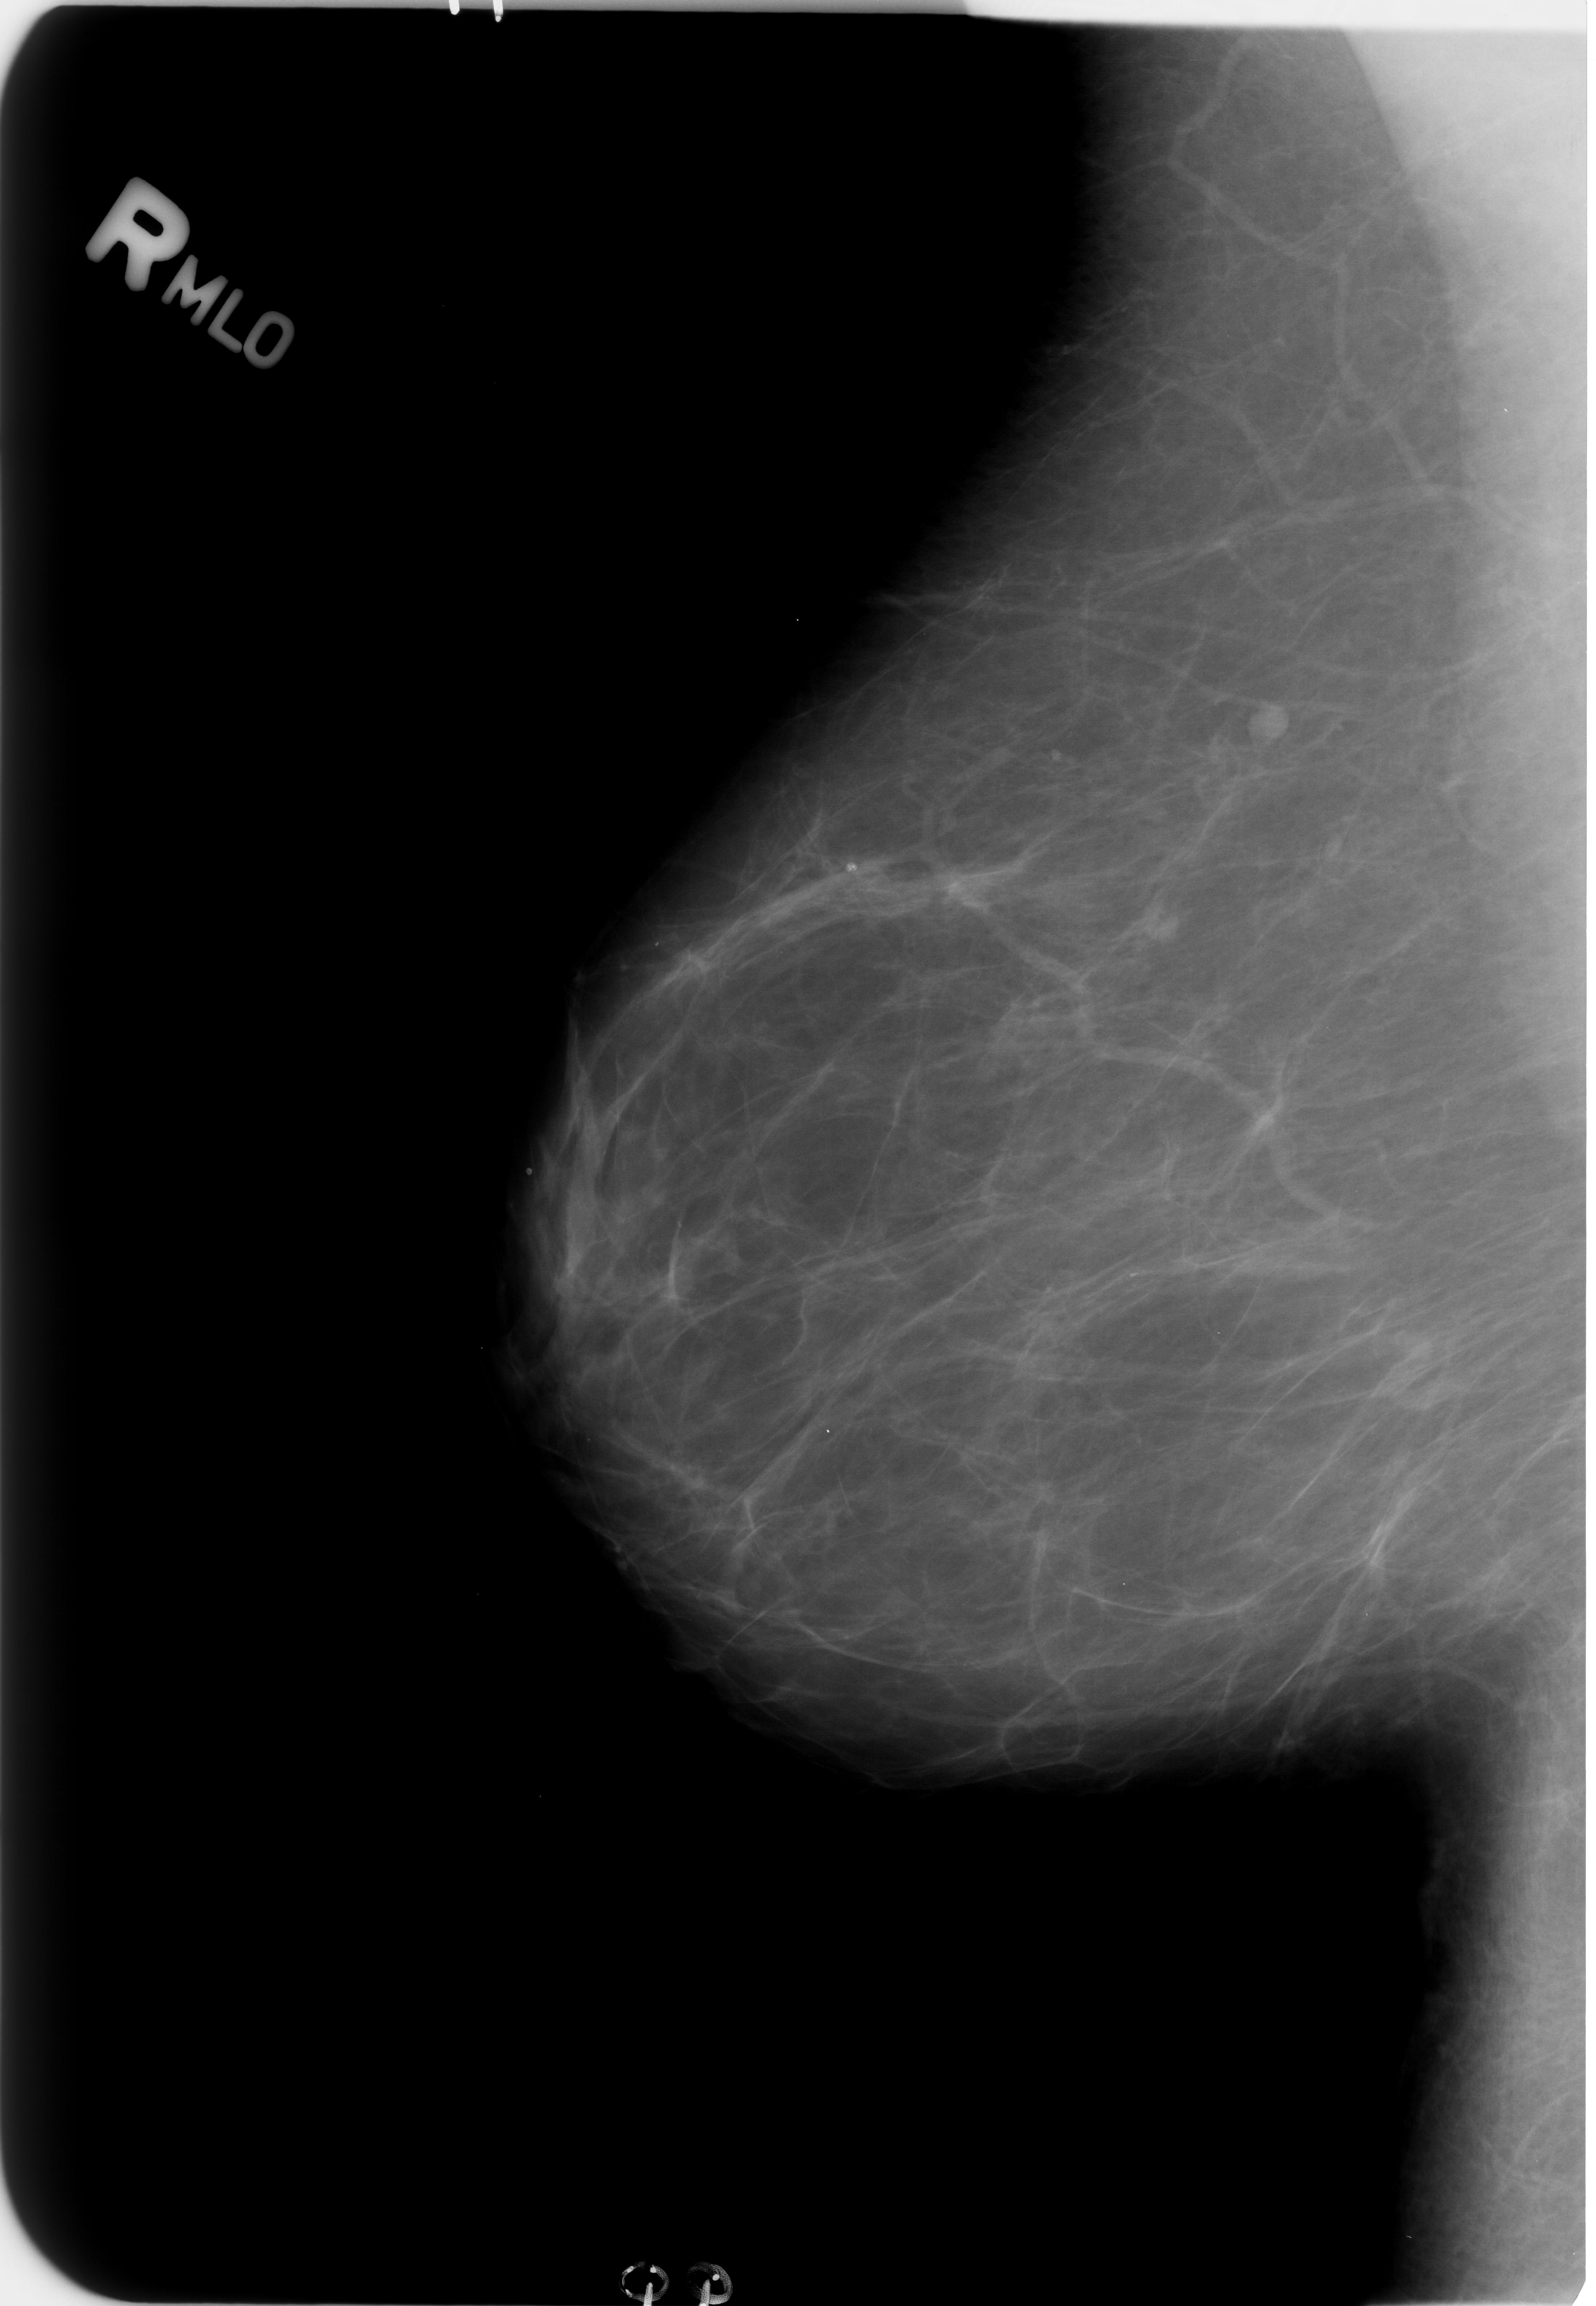
Scanned film-screen mammogram, right breast, MLO view.
Marked findings (only marked abnormalities are described; nothing is implied about the rest of the image): Finding 1 of 3: mass, shape lymph node, margins circumscribed; BI-RADS assessment category 2; subtlety rating 4 on a 1 (subtle) to 5 (obvious) scale; benign; no additional work-up was recommended (benign without callback). Finding 2 of 3: mass, shape lymph node, margins circumscribed; BI-RADS assessment category 2; benign without callback (not worked up further). Finding 3 of 3: mass, shape lymph node, margins circumscribed; BI-RADS assessment category 2; subtlety rating 4 on a 1 (subtle) to 5 (obvious) scale; benign; no additional work-up was recommended (benign without callback).